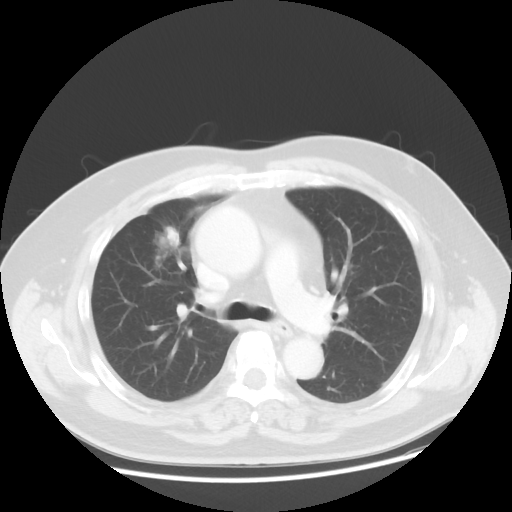
Chest CT, one axial slice. Slice 30 of 48 in the series (ordered by position). Reconstruction kernel STANDARD. Lung window (W 1500 / L -600 HU). 5 mm slice thickness. 512 × 512 image matrix, field of view 392 × 392 mm. Patient: male, 60 years. From the clinical record (not read from this slice): clinical TNM (as recorded): T2 N3 M0; histopathological grade: G2-3.
Outlined on this slice (rectangle marked by the reading radiologist):
- lung tumour (recorded histology: adenocarcinoma): bounding box (x1, y1, x2, y2) in pixels: (139, 218, 192, 280)